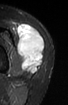
MRI of an extremity soft-tissue mass, one axial slice; STIR; MR volume resampled by the dataset authors to the PET/CT grid (not the native acquisition matrix); 68 × 105 image matrix, field of view 66 × 103 mm. Female patient. Case-level facts recorded for this patient, not image findings: histological type: spindle cell suggestive of biphasic synovial sarcoma; grade: intermediate; site of the primary tumour: left knee.
Annotated regions visible in this slice (expert contour drawn on MRI and transferred to this co-registered scan by the dataset authors):
- gross tumour volume including surrounding oedema: bounding box <14,22,45,73> (left, top, right, bottom; pixels)
- gross tumour volume (mass): <17,24,45,73>